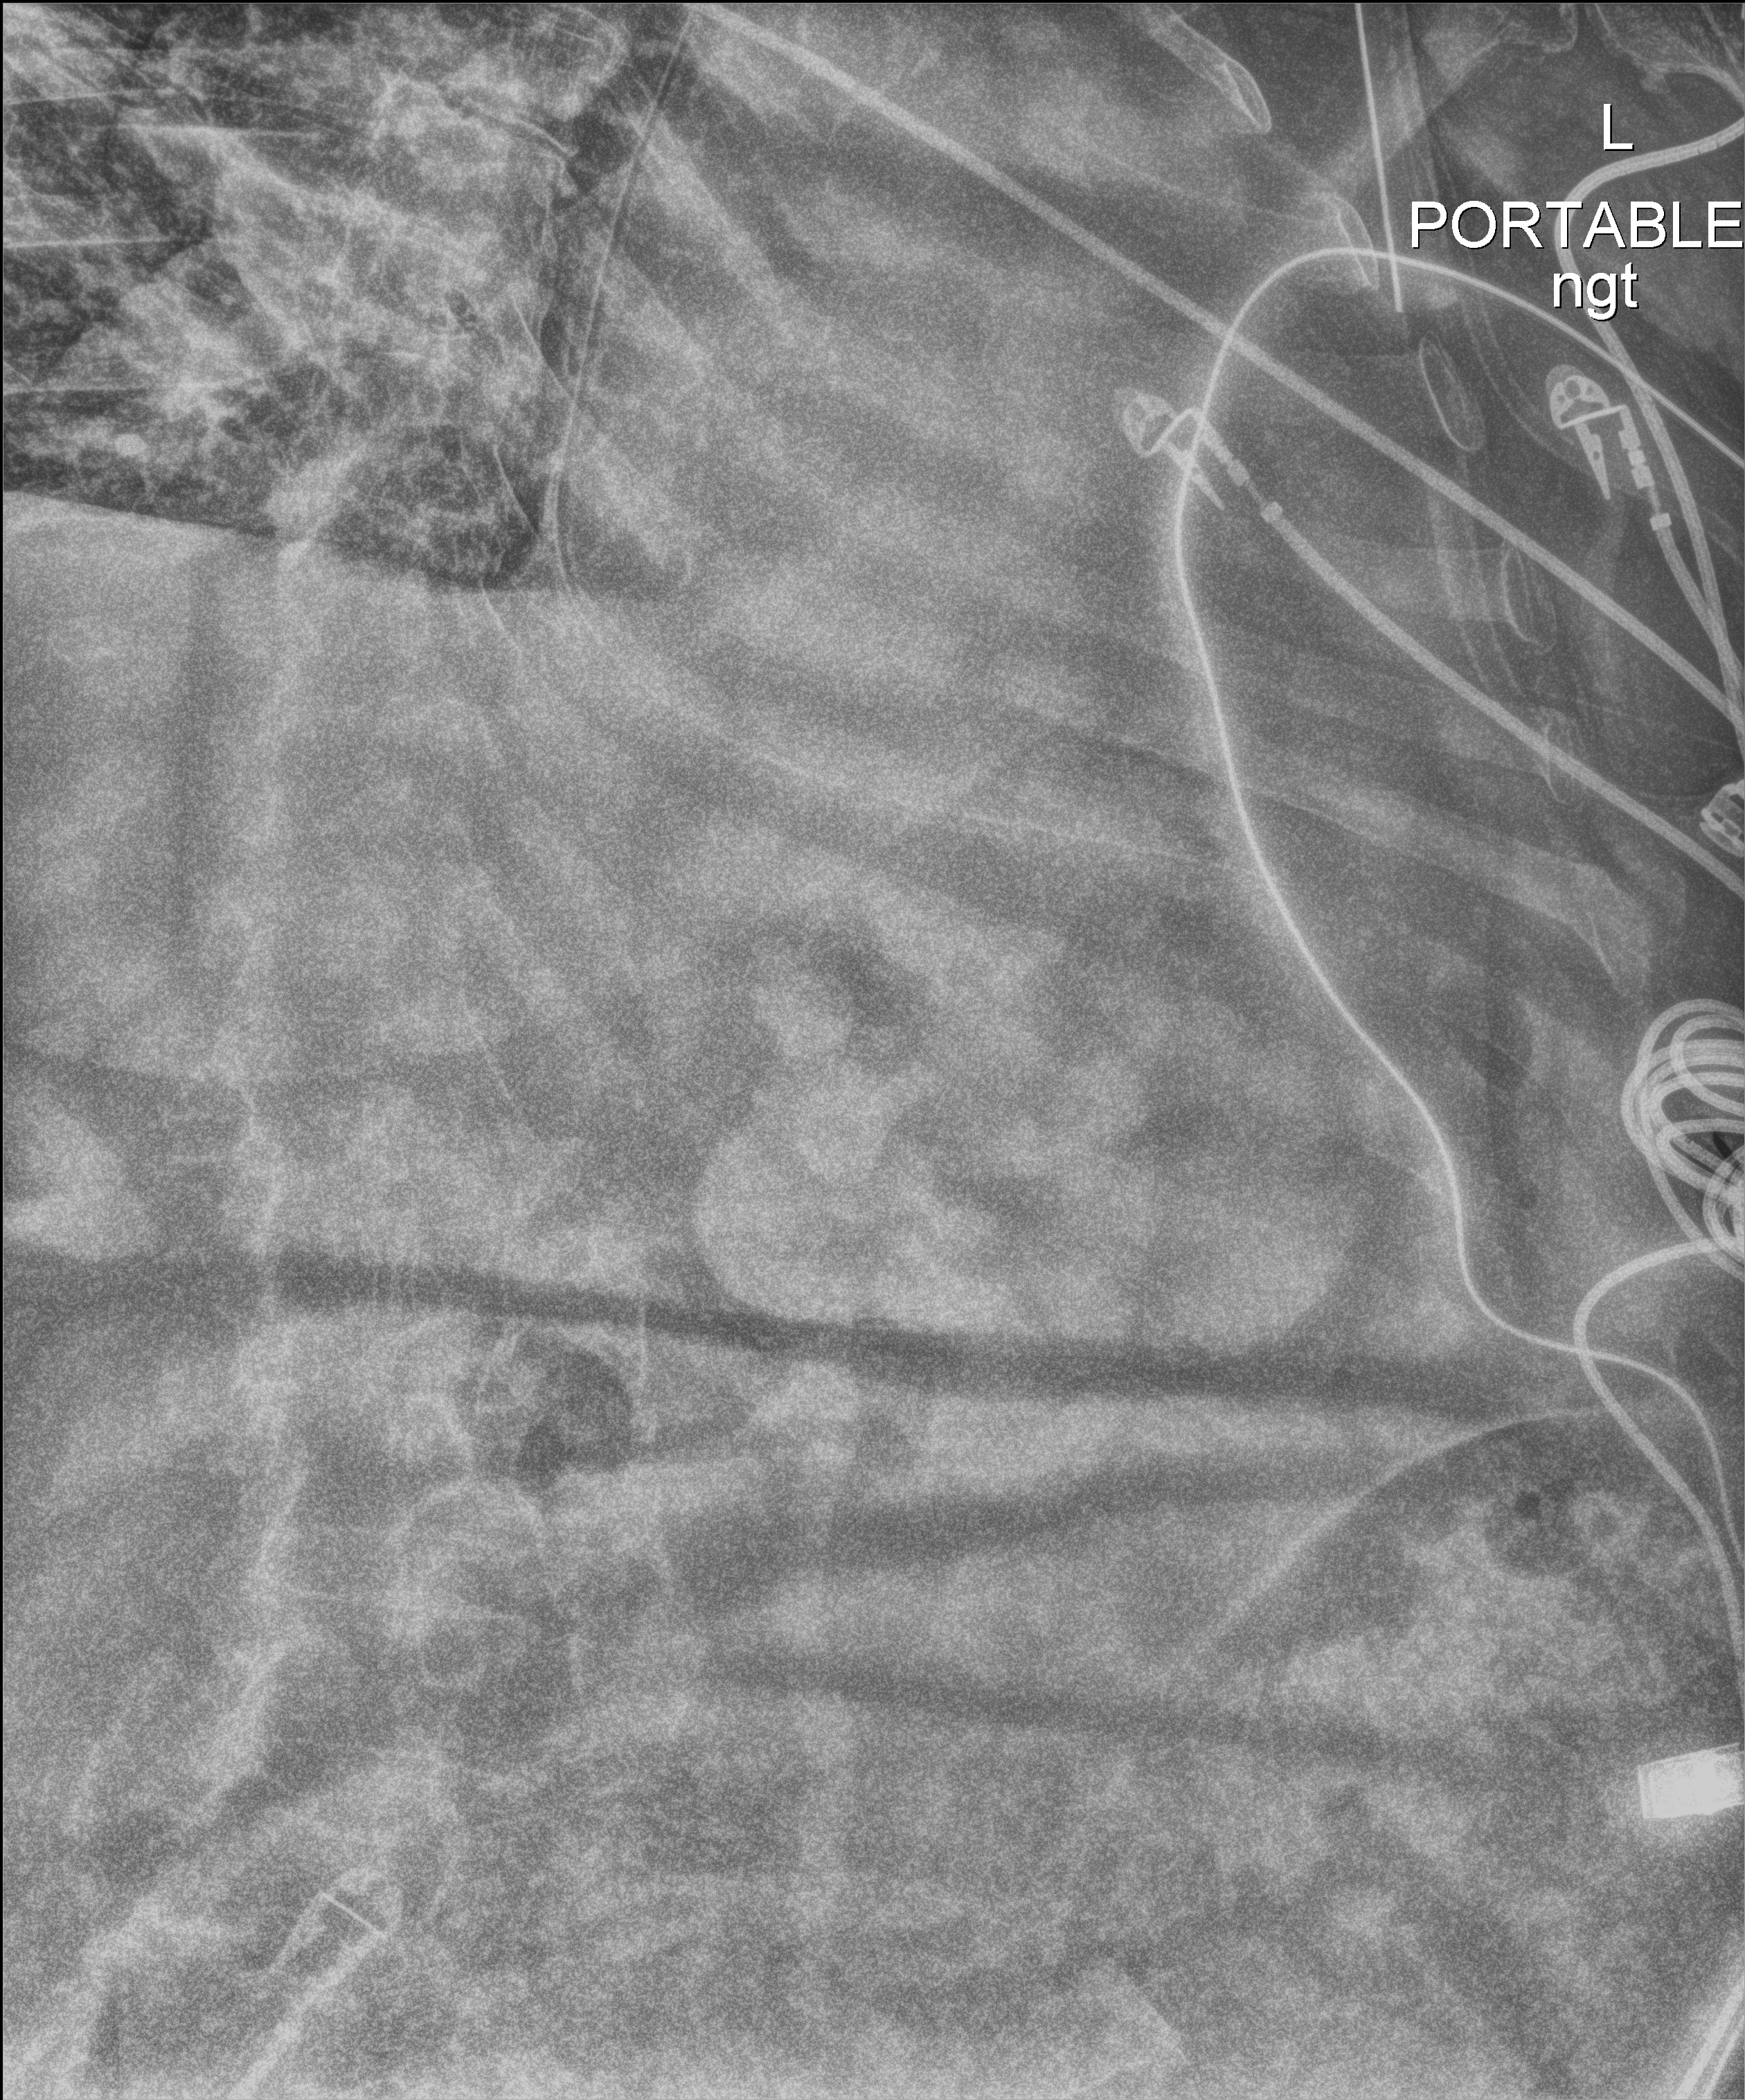
Chest X-ray (portable); anteroposterior (AP) projection. Female patient hospitalised with COVID-19, age 75–90 years.
Hospital-stay facts (about this admission, not read from this image; timing relative to this image not recorded): mechanically ventilated during this hospital stay: no.